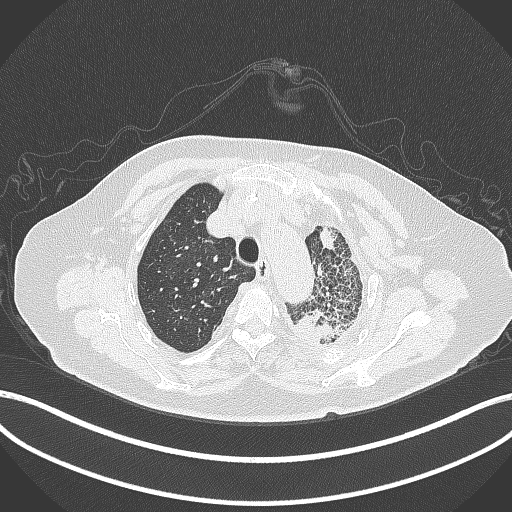
Chest CT, one axial slice. Slice 314 of 399 in the series (ordered by position). Reconstruction kernel B70f. Lung window (W 1500 / L -600 HU). 1 mm slice thickness. 512 × 512 image matrix. Female patient, age 75 years. Case-level facts recorded for this patient, not image findings: clinical TNM (as recorded): T3 N3 M1.
Outlined on this slice (bounding box drawn by a radiologist):
- lung tumour (recorded histology: adenocarcinoma): bounding box [x1, y1, x2, y2] px = [295, 306, 350, 346]